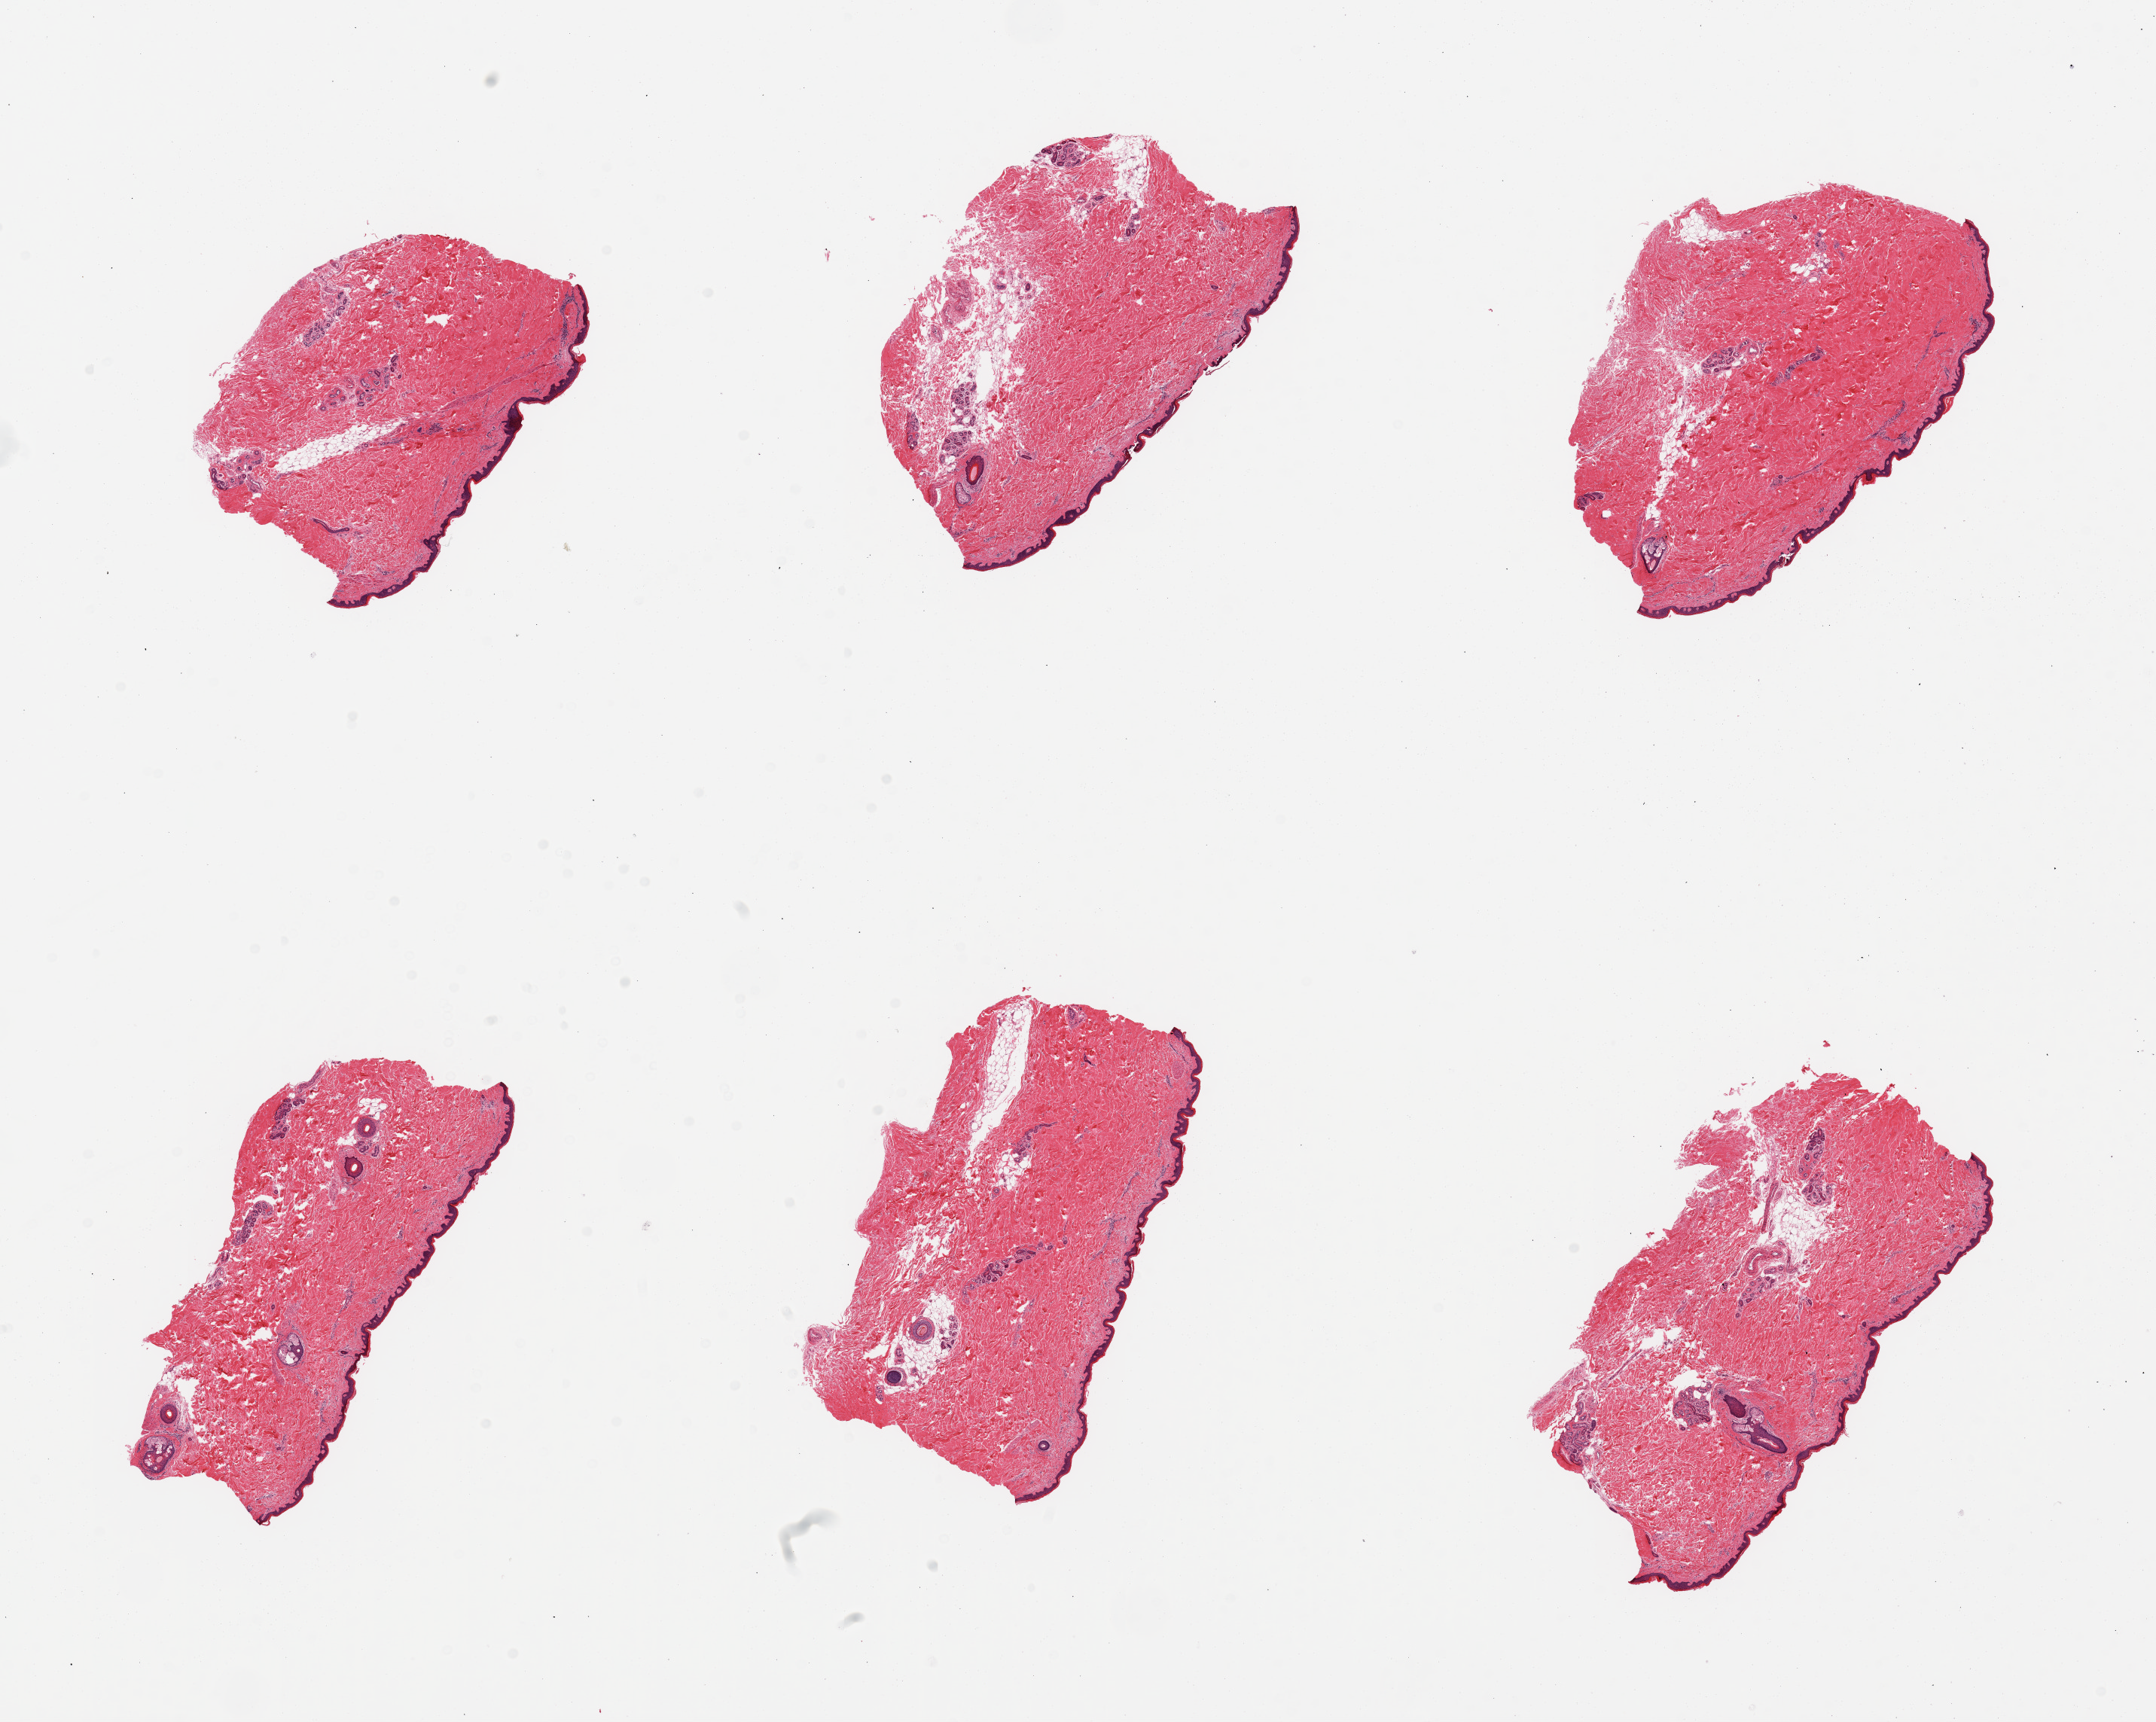
Whole-slide image, haematoxylin and eosin stain, brightfield — a low-resolution overview of the entire scanned area, about 22.6 x 18.1 mm; PAXgene-fixed, paraffin-embedded tissue; sampled site (target tissue): skin of lower leg; donor tissue sample. Donor: male.
Reviewer comment on this tissue sample: 6 pieces; well trimmed; 10% intradermal fat.